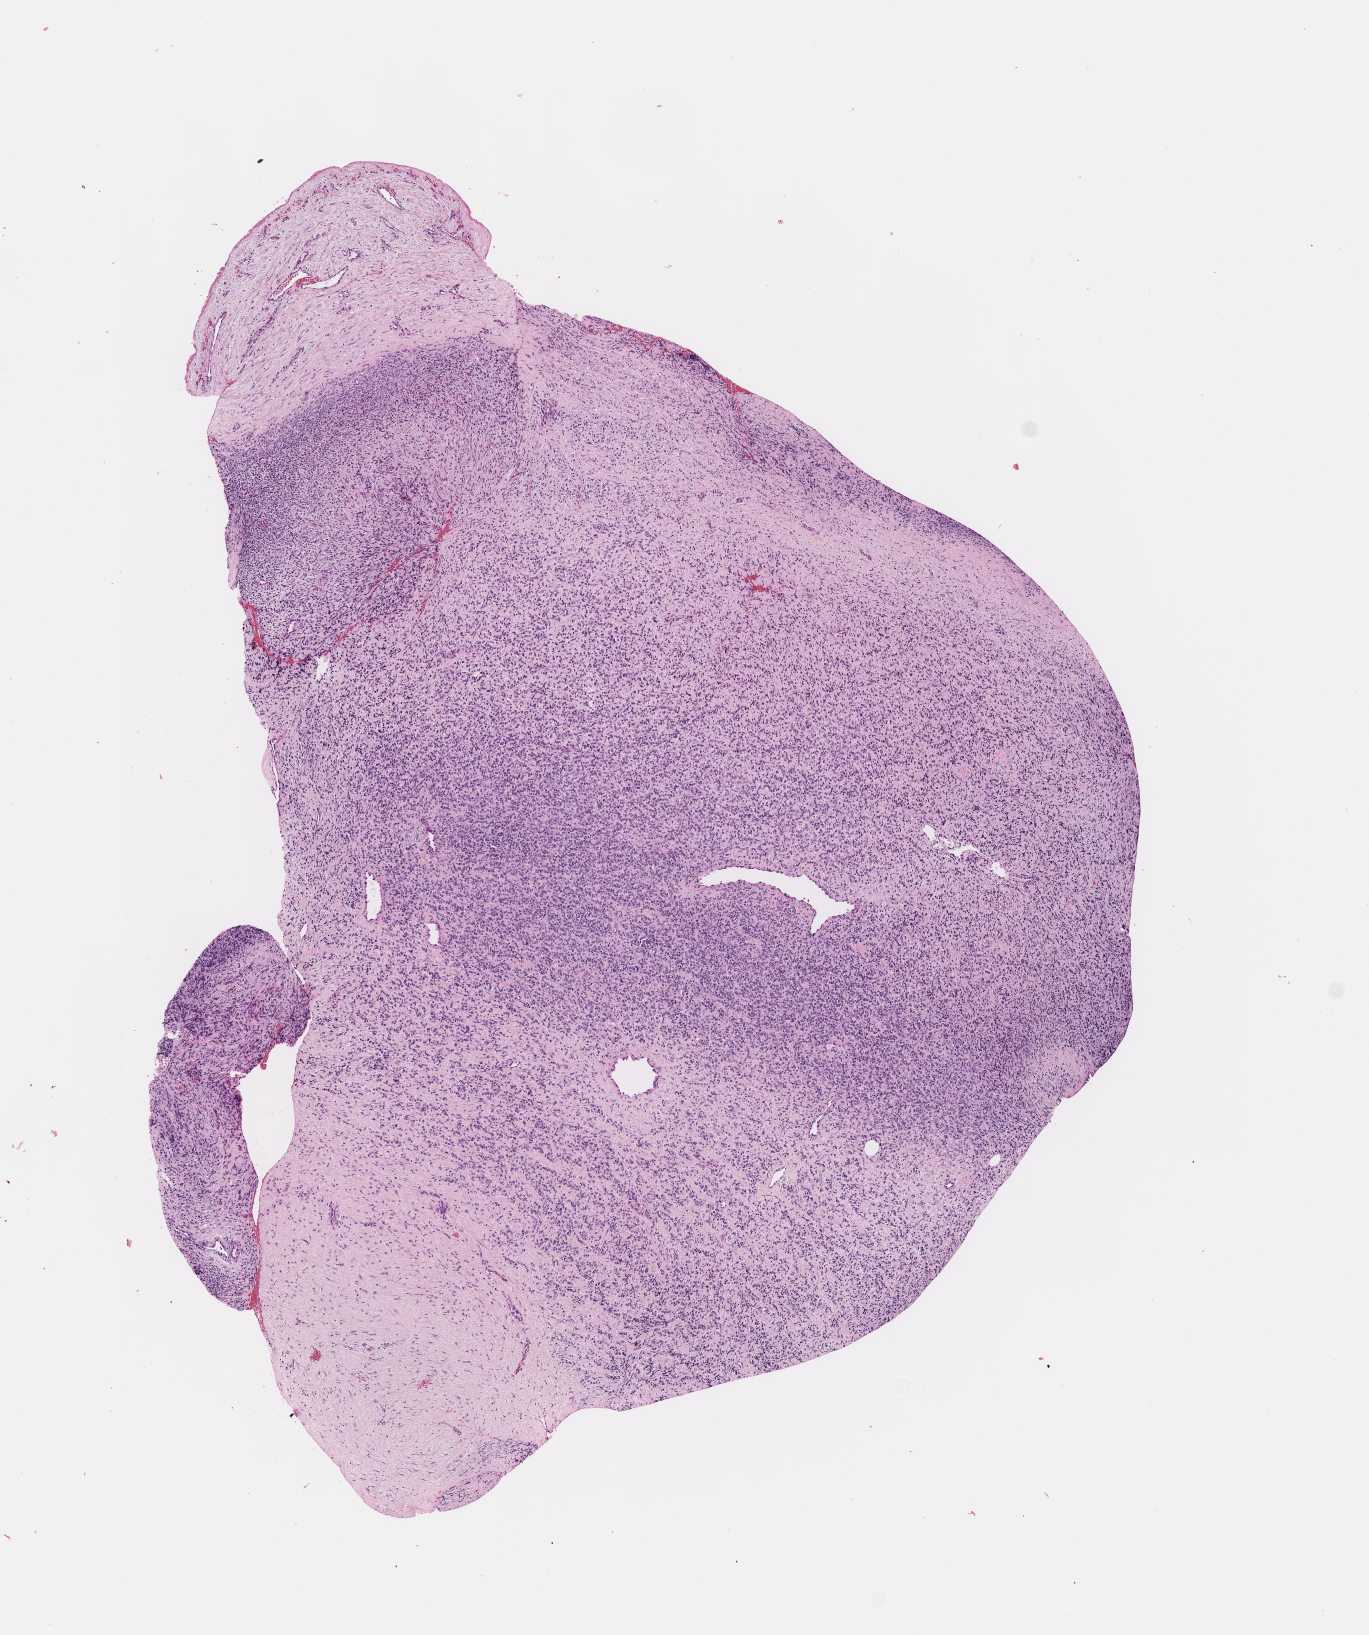
Whole-slide image, hematoxylin and eosin (H&E) stain of tumor tissue, low-resolution overview of the scanned area, about 5.5 x 6.6 mm, FFPE section, site: abdomen. Patient: male, age 1.3 years at diagnosis.
Diagnosis: rhabdomyosarcoma; histological classification: embryonal rhabdomyosarcoma. Metastatic status at presentation (as recorded): non-metastatic. Stage (as recorded): 3.